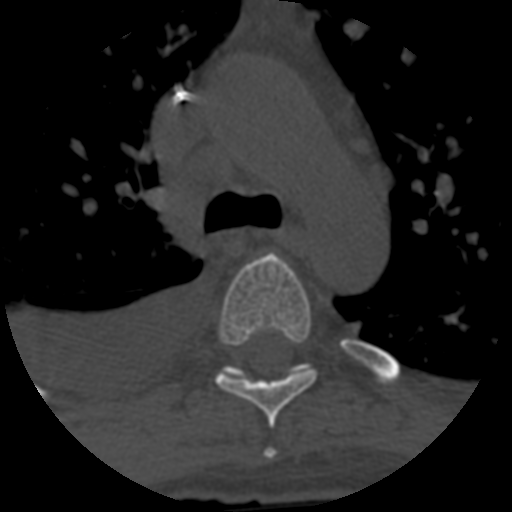
CT including the spine, one axial slice; position 451 of 708 along the scan axis; one of 3 acquisitions stored at this slice position; bone window (W 1800 / L 400 HU); 1.25 mm slice thickness; 512 × 512 image matrix, field of view 160 × 160 mm. Patient age 55 years. From the clinical record (not read from this slice): primary cancer: colon.
Outlined on this slice (semi-automatic segmentation, software-assisted and operator-edited):
- T4 vertebra: box from (x=263, y=449) to (x=276, y=459) px
- T5 vertebra: (x=215, y=254)–(x=317, y=428)
- T6 vertebra: (x=222, y=364)–(x=313, y=377)